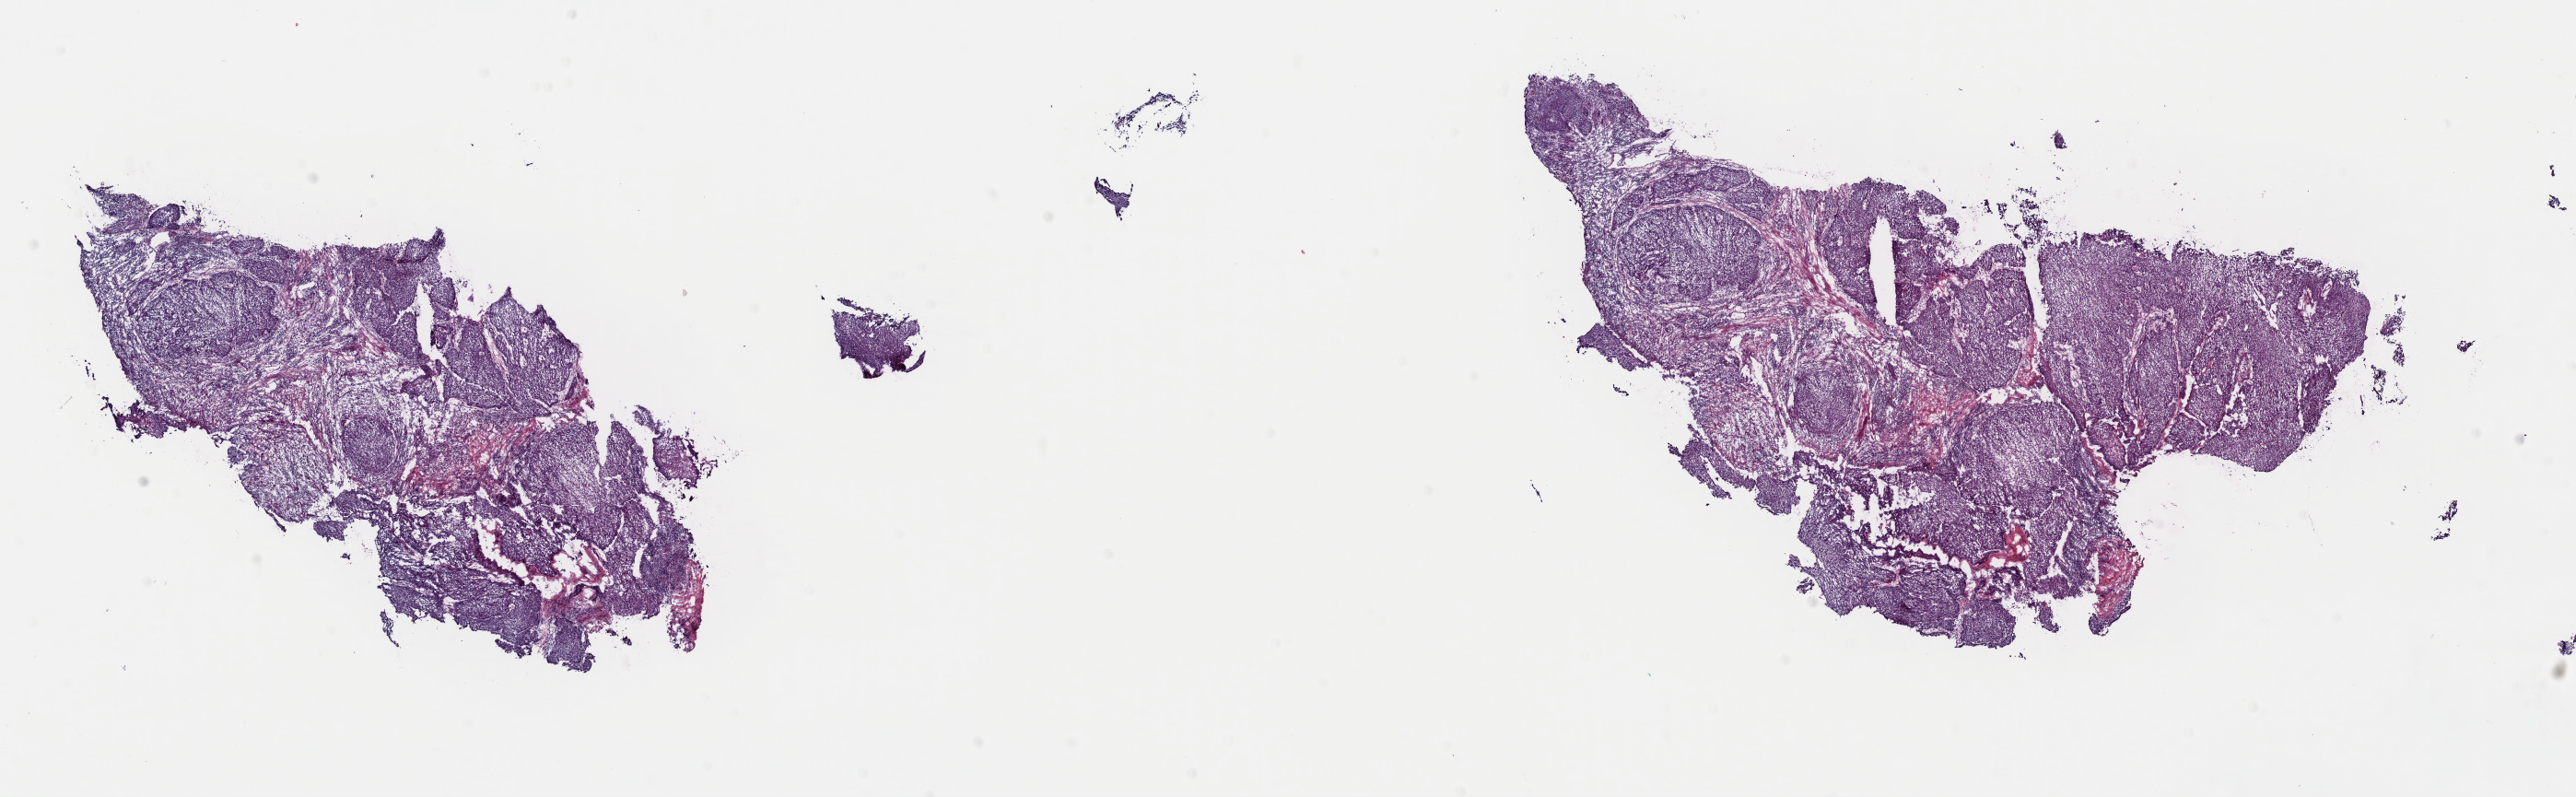
Digitized H&E tissue section (whole slide), shown as a low-resolution overview of the whole scanned area (about 22.1 x 6.8 mm, acquisition: 40x scan). Frozen section. Head and neck, primary tumour sample. Male, age 63 years at initial diagnosis. Histologic grade: G2 (moderately differentiated). Composition of this section per pathologist review: tumour cells 80%, tumour nuclei 80%, normal cells 15%, stromal cells 5%, necrosis 0%. Inflammatory infiltration, as recorded: lymphocyte infiltration 30%, monocyte infiltration 0%, neutrophil infiltration 0%.
• pathologic diagnosis: Squamous cell carcinoma, large cell, nonkeratinizing, NOS
• AJCC pathologic stage: III (7th edition)